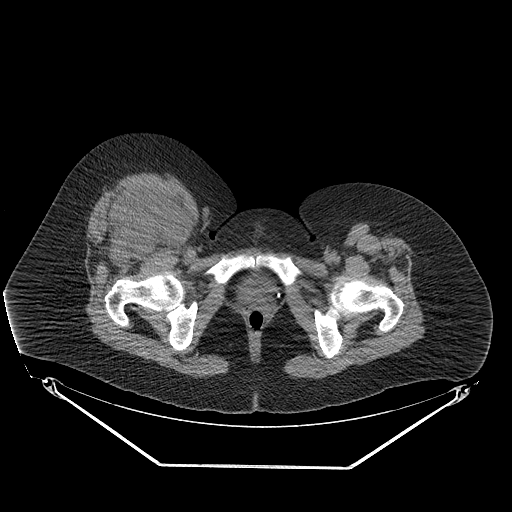
CT of an extremity soft-tissue mass (from a PET/CT study), one axial slice. Slice 62 of 267 in the series (ordered by position). 140 kVp. Soft-tissue window (W 400 / L 40 HU). 3.75 mm slice thickness. 512 × 512 image matrix. Female patient. From the clinical record (not read from this slice): histological type: malignant solitary fibrous tumor; grade: intermediate; site of the primary tumour: right thigh.
Structures marked on this image (expert contour drawn on MRI and transferred to this co-registered scan by the dataset authors):
- gross tumour volume including surrounding oedema: bounding box <101,185,175,243> (left, top, right, bottom; pixels)
- gross tumour volume (mass): <119,190,168,227>